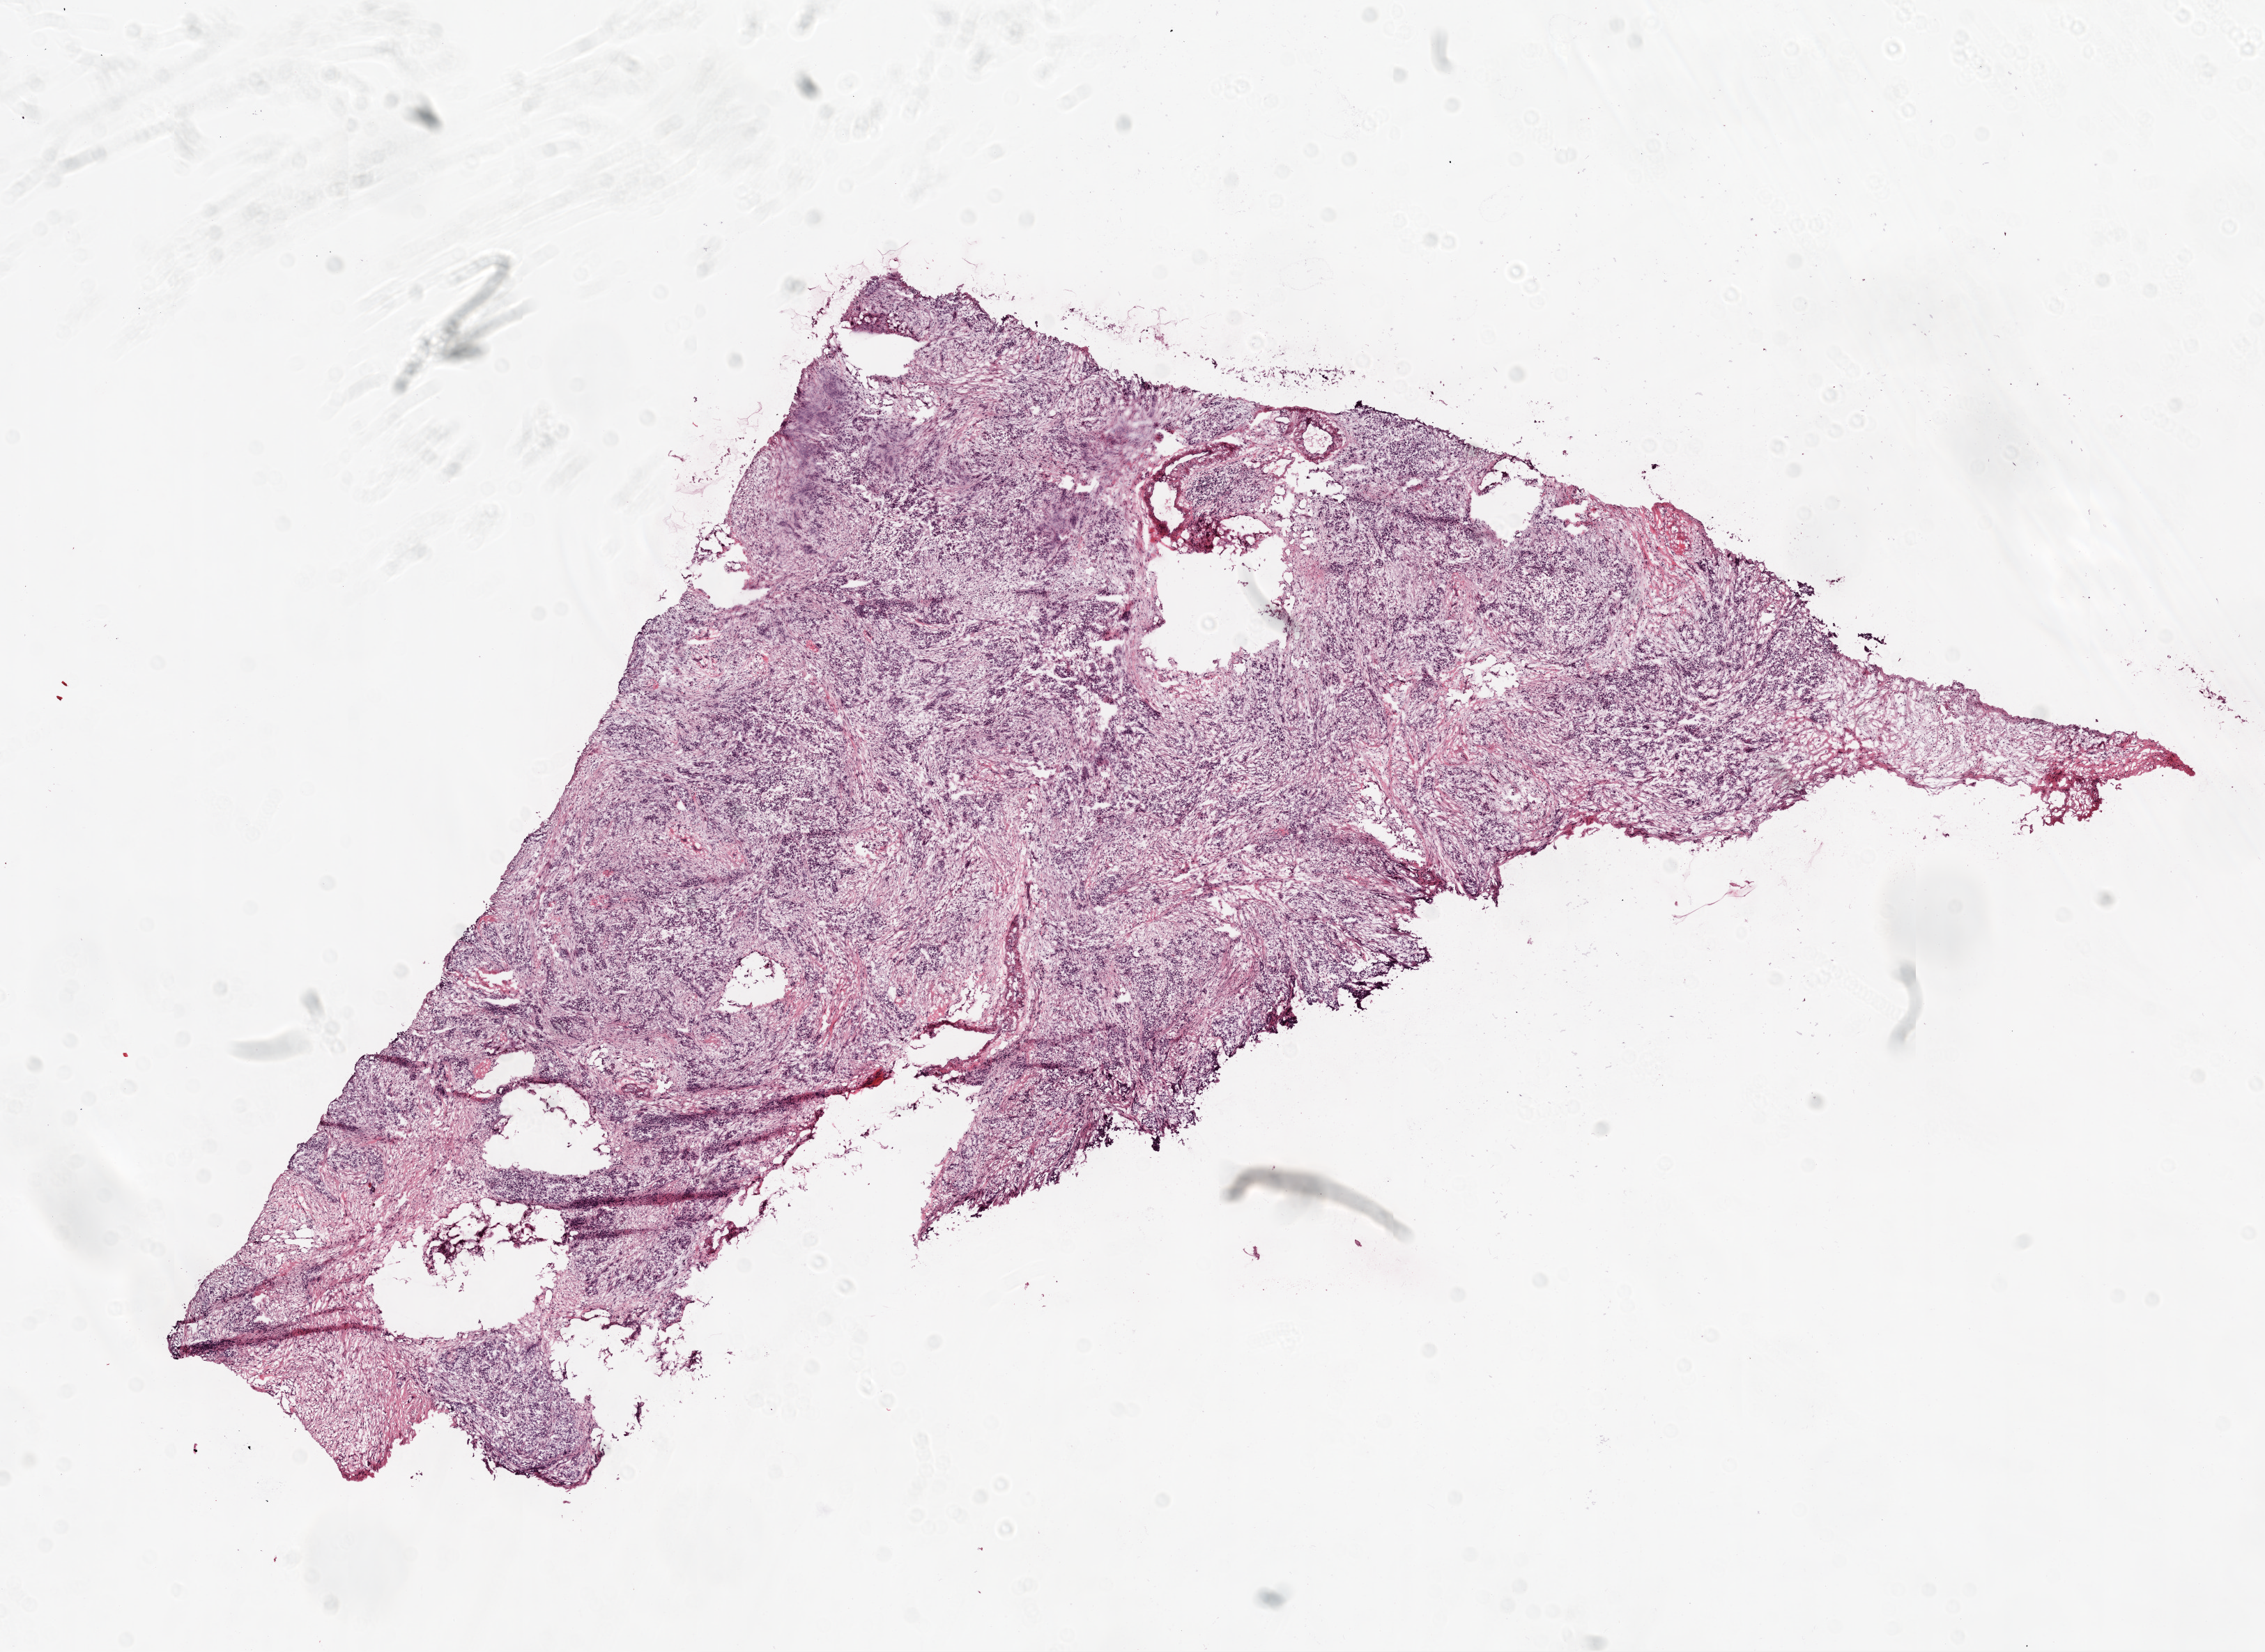
H&E whole-slide image, whole scanned area (about 13.0 x 9.5 mm) shown as a low-resolution overview; frozen section; ovary, primary tumour sample. Female, age 50 years at initial diagnosis. Histologic grade: G3 (poorly differentiated). Composition of this section per pathologist review: tumour cells 50%, tumour nuclei 90%, normal cells 0%, stromal cells 50%, necrosis 0%.
• FIGO stage: IV
• pathologic diagnosis: Serous cystadenocarcinoma, NOS
• laterality: bilateral